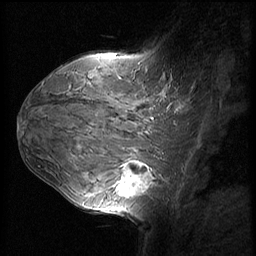
Breast MRI (dynamic contrast-enhanced), one sagittal slice. Position 38 of 60 along the scan axis. Dynamic contrast-enhanced series, image 2 of 3 at this slice position (ordered by acquisition). 1.5 T. TE 4.2 ms, TR 8.9 ms. 2.5 mm slice thickness. 256 × 256 image matrix, field of view 220 × 220 mm. Patient: female, 37 years. From the clinical record (not read from this slice): setting: breast cancer imaged before/during neoadjuvant chemotherapy; receptor status: triple-negative.
Structures marked on this image (semi-automatically segmented with operator editing):
- analysis volume of interest (the breast-tissue region the enhancement analysis was run in; not a lesion): bounding box (x1, y1, x2, y2) in pixels: (114, 153, 159, 206)
- tumour enhancement mask (voxels above the 140 % enhancement threshold inside the analysis volume of interest): (118, 162, 153, 198)